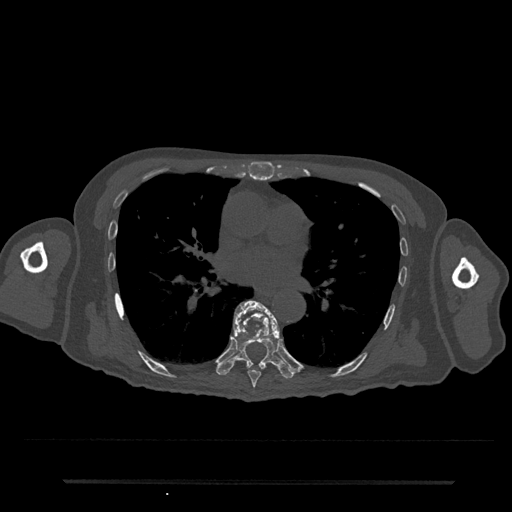
CT including the spine, one axial slice. Reconstruction kernel Br40s/3. 120 kVp. Bone window (W 1800 / L 400 HU). 0.5 mm slice thickness. 512 × 512 image matrix. Male patient, age 74 years. Case-level facts recorded for this patient, not image findings: primary cancer: prostate.
Structures marked on this image (semi-automatically segmented with operator editing):
- T7 vertebra: bounding box [x1, y1, x2, y2] px = [233, 301, 280, 388]
- T8 vertebra: [216, 300, 295, 379]